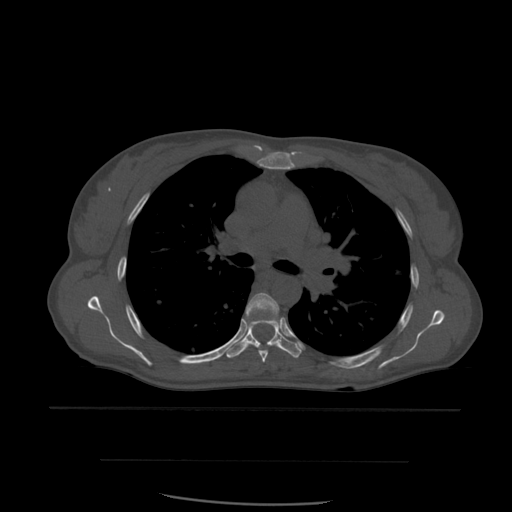
CT including the spine, one axial slice. Position 400 of 574 along the scan axis. Bone window (W 1800 / L 400 HU). 1.25 mm slice thickness. 512 × 512 image matrix, field of view 392 × 392 mm. Patient age 48 years. From the clinical record (not read from this slice): primary cancer: lung; vertebrae with lytic lesions (as recorded): T11.
Outlined on this slice (semi-automatically segmented with operator editing):
- T5 vertebra: bounding box <246,293,281,363> (left, top, right, bottom; pixels)
- T6 vertebra: <227,318,302,359>